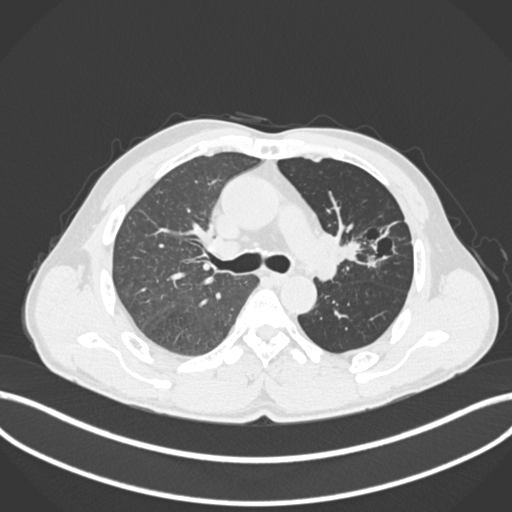
Chest CT, one axial slice; position 123 of 255 along the scan axis; reconstruction kernel B30f; 120 kVp; lung window (W 1500 / L -600 HU); 1 mm slice thickness; 512 × 512 image matrix. Male patient, age 57 years. Case-level facts recorded for this patient, not image findings: clinical TNM (as recorded): T2b N0 M0.
Annotated regions visible in this slice (bounding box drawn by a radiologist):
- lung tumour (recorded histology: squamous cell carcinoma): bounding box (x1, y1, x2, y2) in pixels: (319, 224, 368, 269)